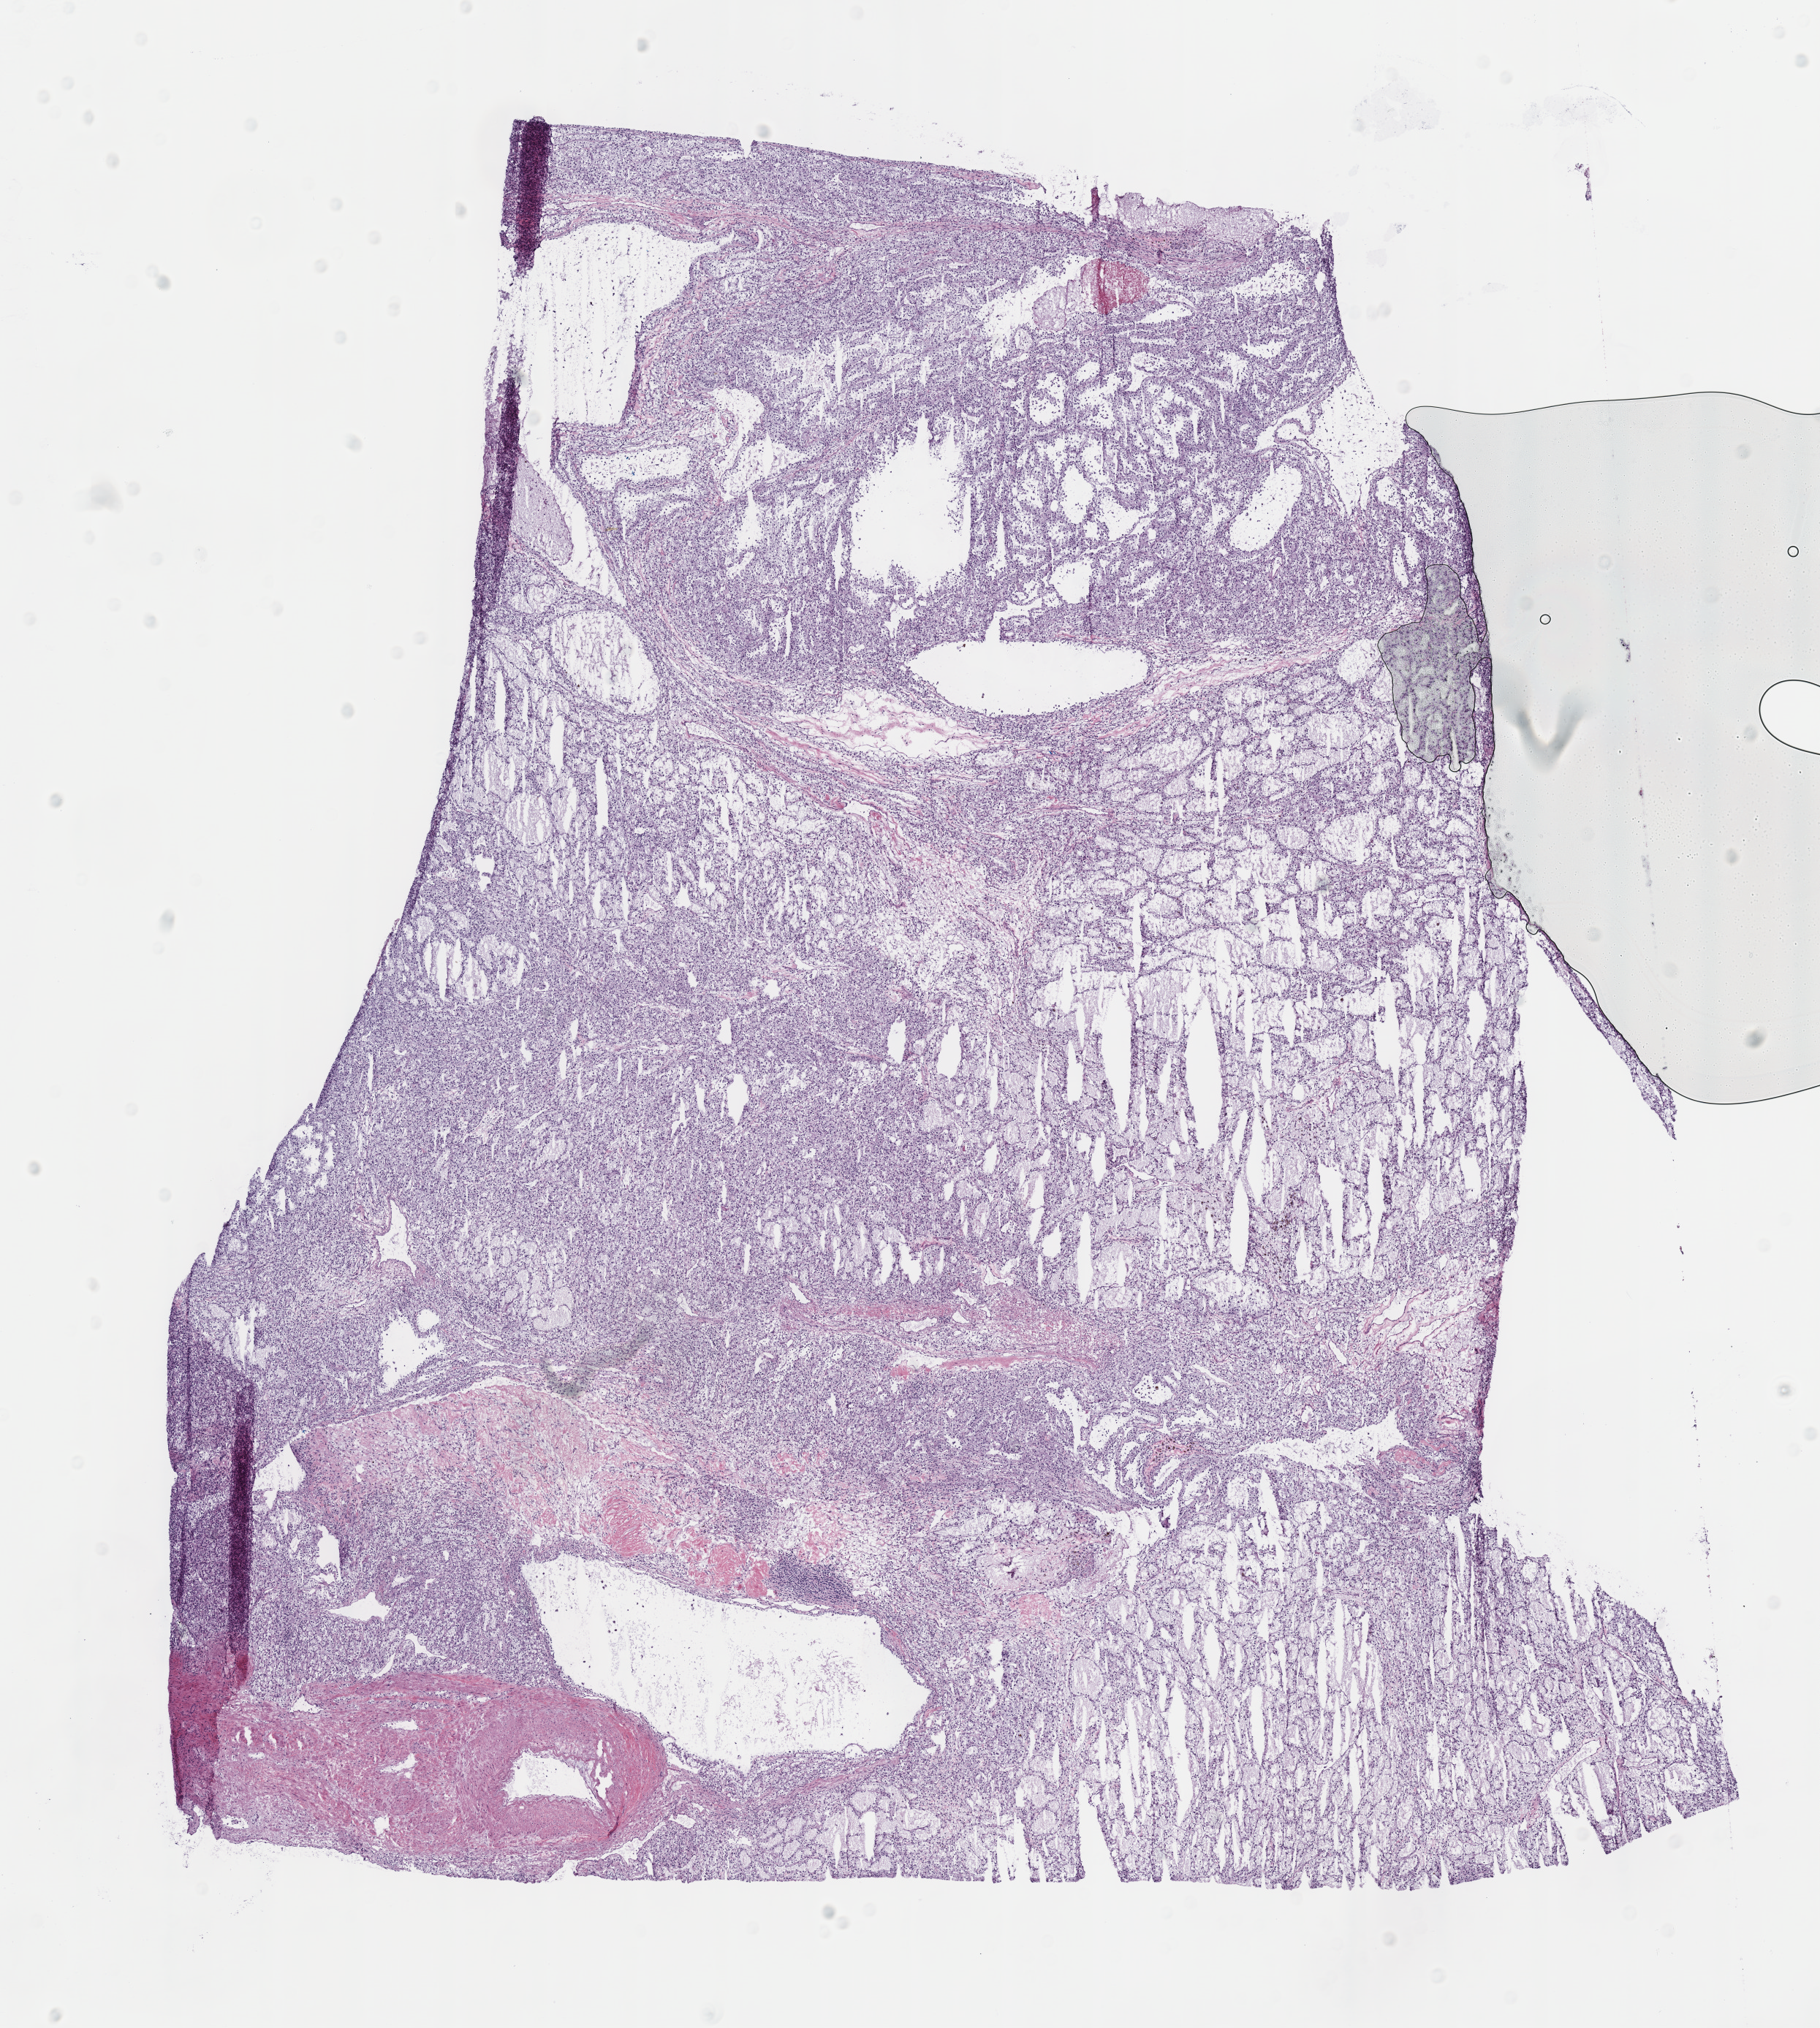
Digitized Hematoxylin and eosin (H&E) stained tissue section (whole slide) — a low-resolution overview of the entire scanned area, about 9.8 x 10.9 mm (slide scanned at 40x), frozen section, sample: primary tumour, kidney. Female, age 67 years at initial diagnosis. Histologic grade: G2 (moderately differentiated). Composition of this section per pathologist review: tumour cells 88%, tumour nuclei 85%, normal cells 0%, stromal cells 10%, necrosis 2%.
* AJCC pathologic stage: I
* TNM: T1b N0 M0
* laterality: left
* histologic diagnosis: Clear cell adenocarcinoma, NOS